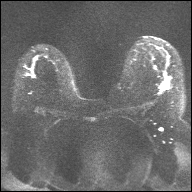
Breast MRI, one axial slice. Diffusion-weighted series; image 2 of 4 stored at this slice position (different b-values; order by instance number). 1.5 T. 4 mm slice thickness. 192 × 192 image matrix, field of view 360 × 360 mm. Female patient.
Structures marked on this image (outlined manually by an expert reader):
- tumour on diffusion-weighted imaging: bounding box <164,83,168,88> (left, top, right, bottom; pixels)